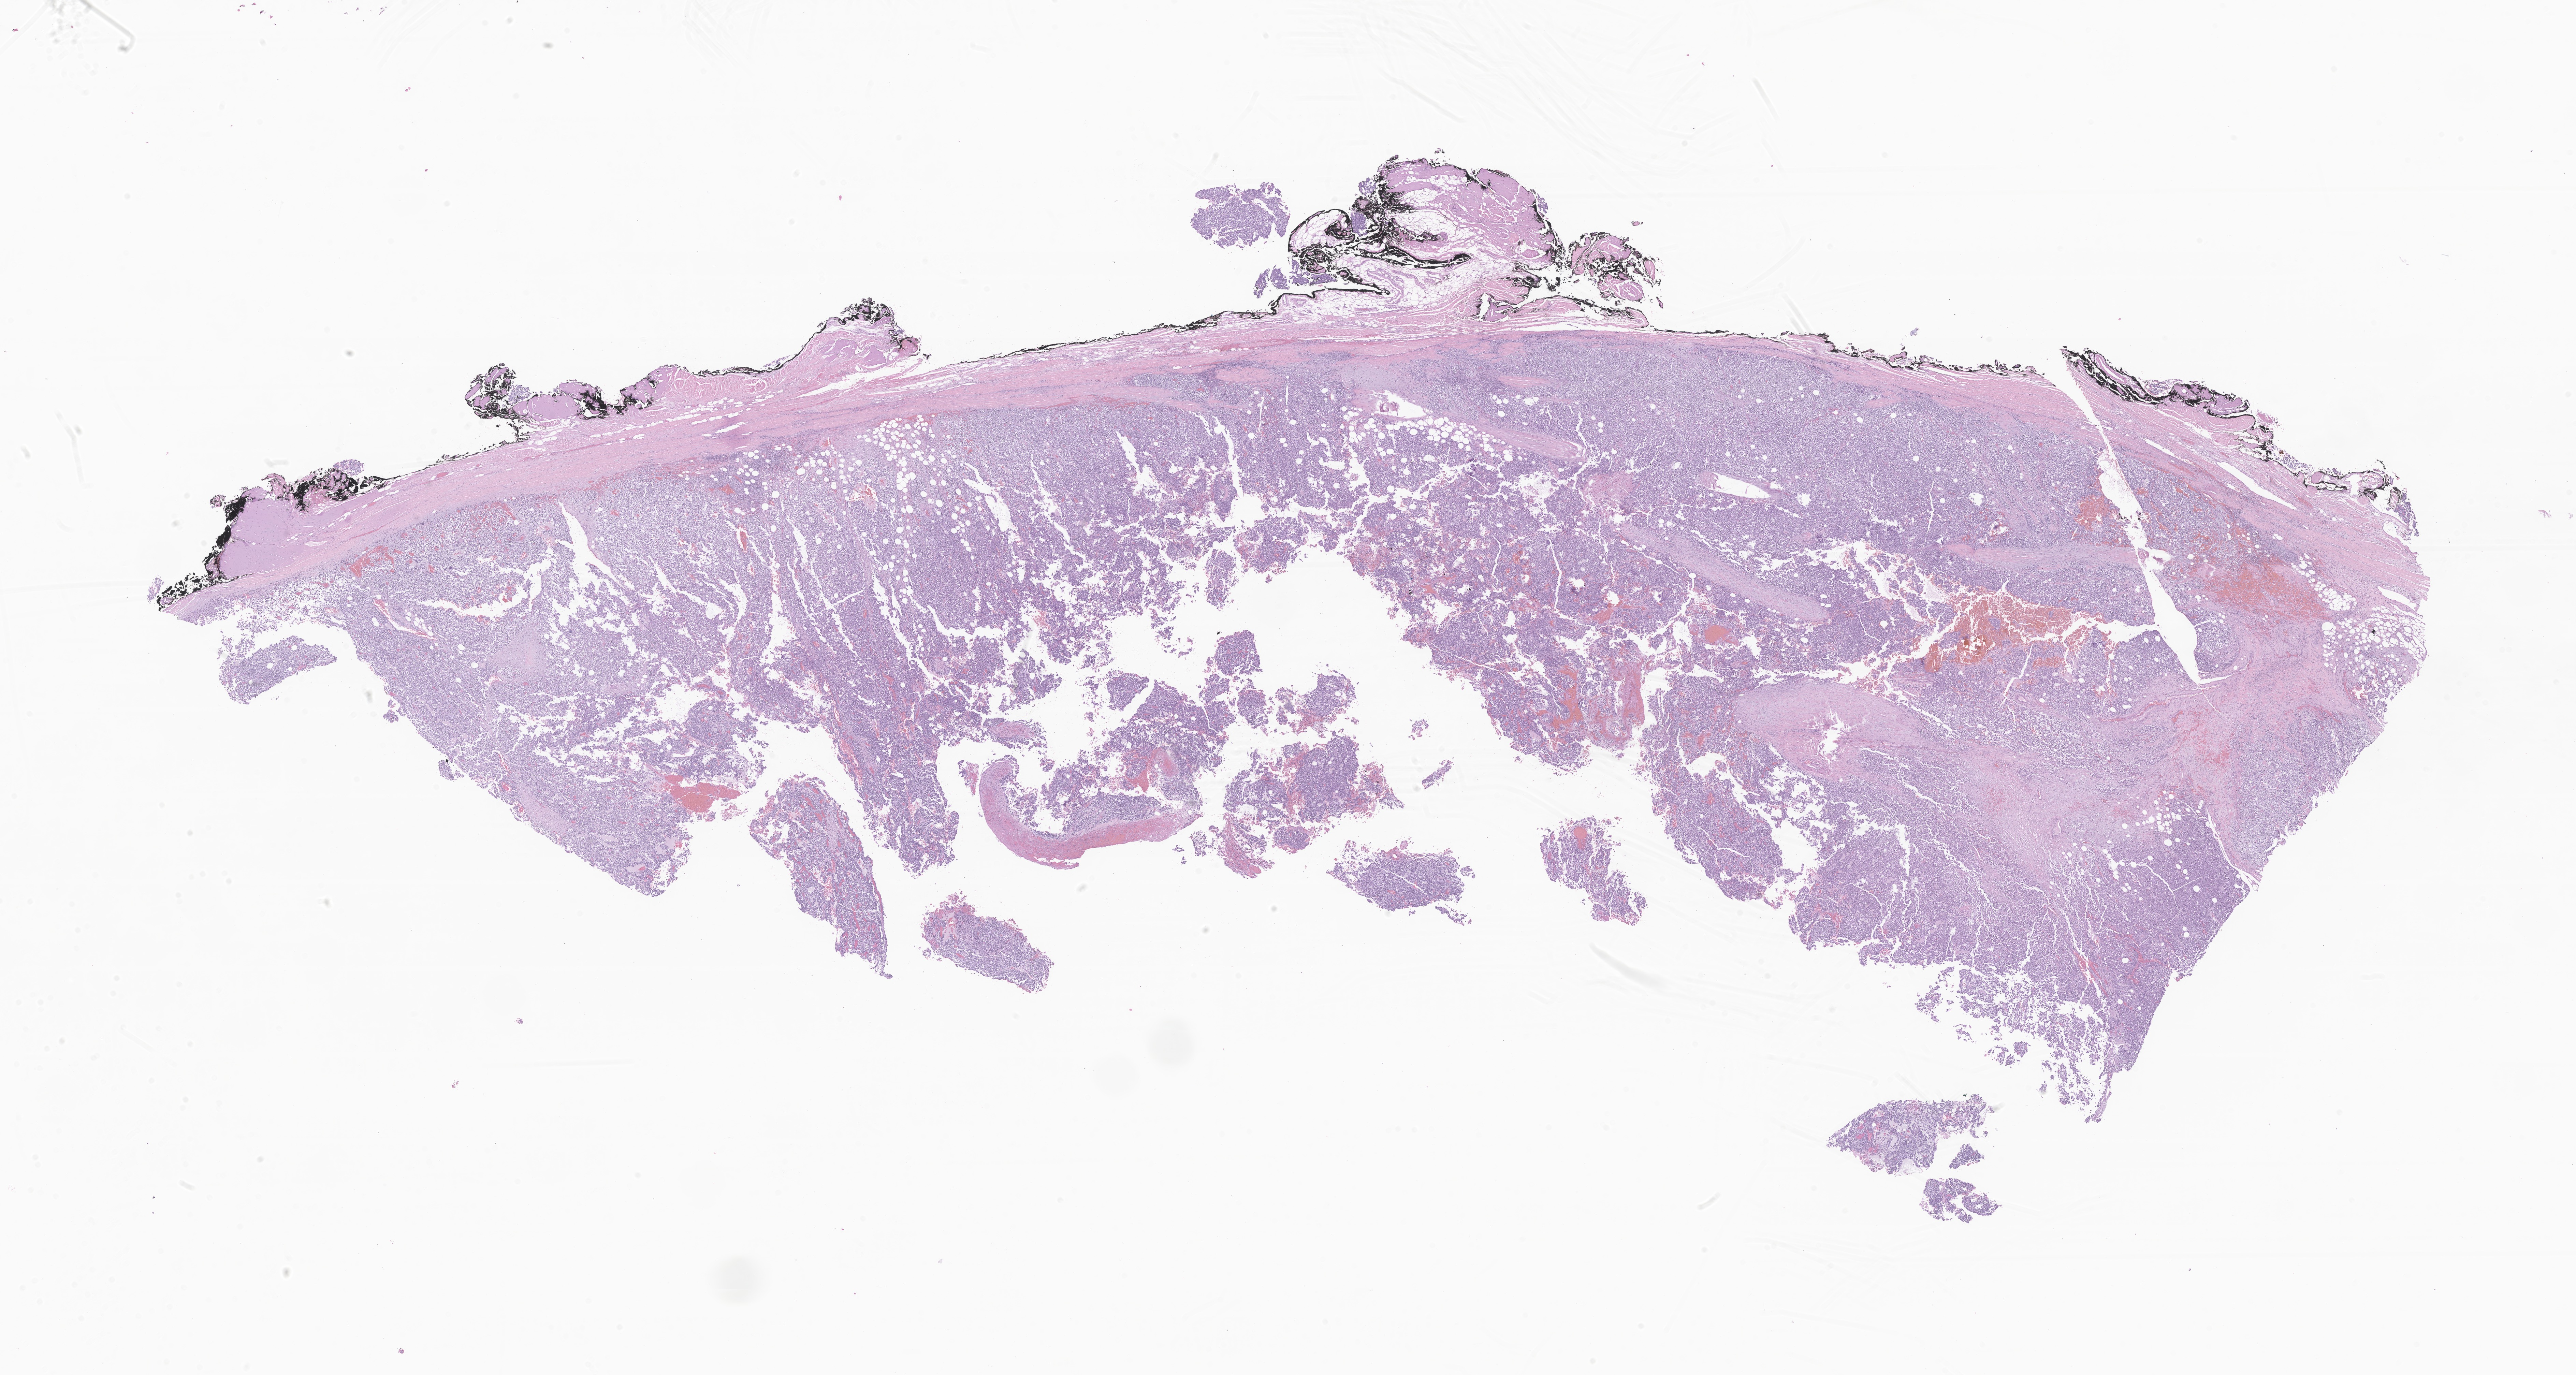
Haematoxylin and eosin whole-slide image of tumor tissue from the soft tissue, whole scanned area (about 31.8 x 17.0 mm) shown as a low-resolution overview; formalin-fixed paraffin-embedded section. Female patient, age 126 months.
Diagnosis (ICD-O-3 morphology term): Sarcoma, NOS.